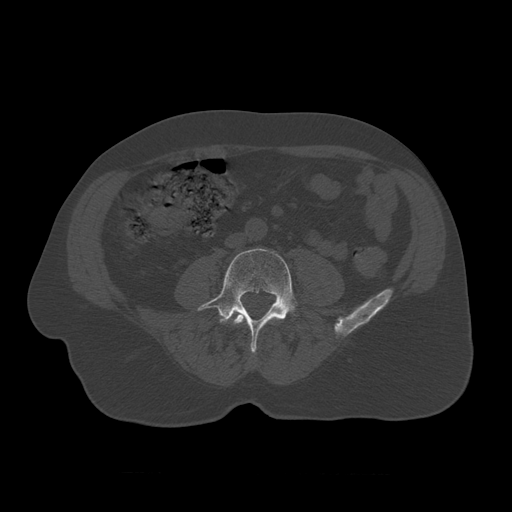
CT including the spine, one axial slice; slice 279 of 450 in the series (ordered by position); reconstruction kernel STANDARD; 120 kVp; bone window (W 1800 / L 400 HU); 1.25 mm slice thickness; 512 × 512 image matrix, field of view 405 × 405 mm. Patient age 75 years. Case-level facts recorded for this patient, not image findings: primary cancer: prostate.
Annotated regions visible in this slice (semi-automatic segmentation, software-assisted and operator-edited):
- L3 vertebra: bounding box [x1, y1, x2, y2] px = [234, 313, 245, 325]
- L4 vertebra: [198, 248, 298, 355]
- L5 vertebra: [230, 318, 234, 324]